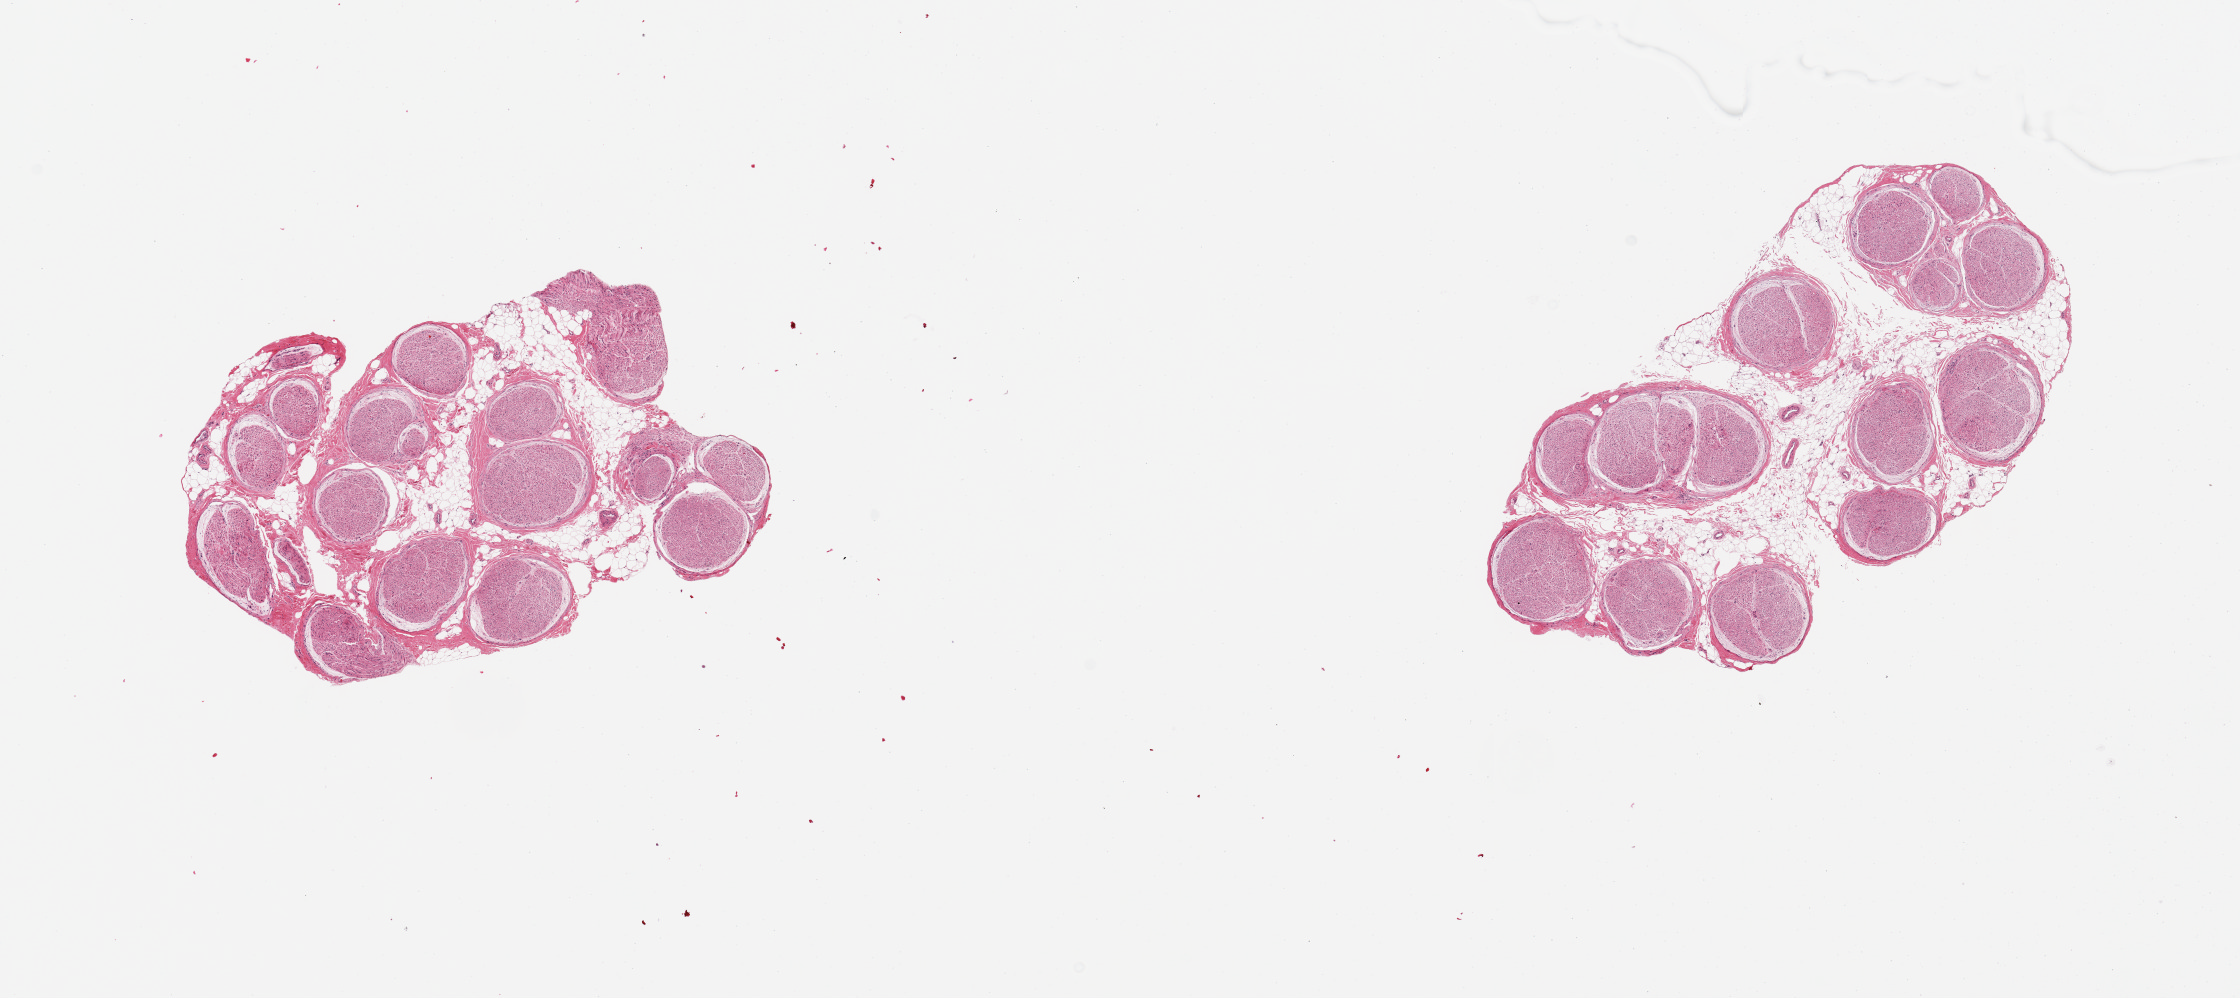
Whole-slide image, haematoxylin and eosin stain, brightfield, a low-resolution overview of the entire scanned area, about 17.7 x 7.9 mm; PAXgene-fixed paraffin-embedded (PFPE) section; section of tibial nerve (target tissue); tissue donor sample. Donor: female.
* review note (as recorded): 2 pieces, good celan sections, no adherent fat